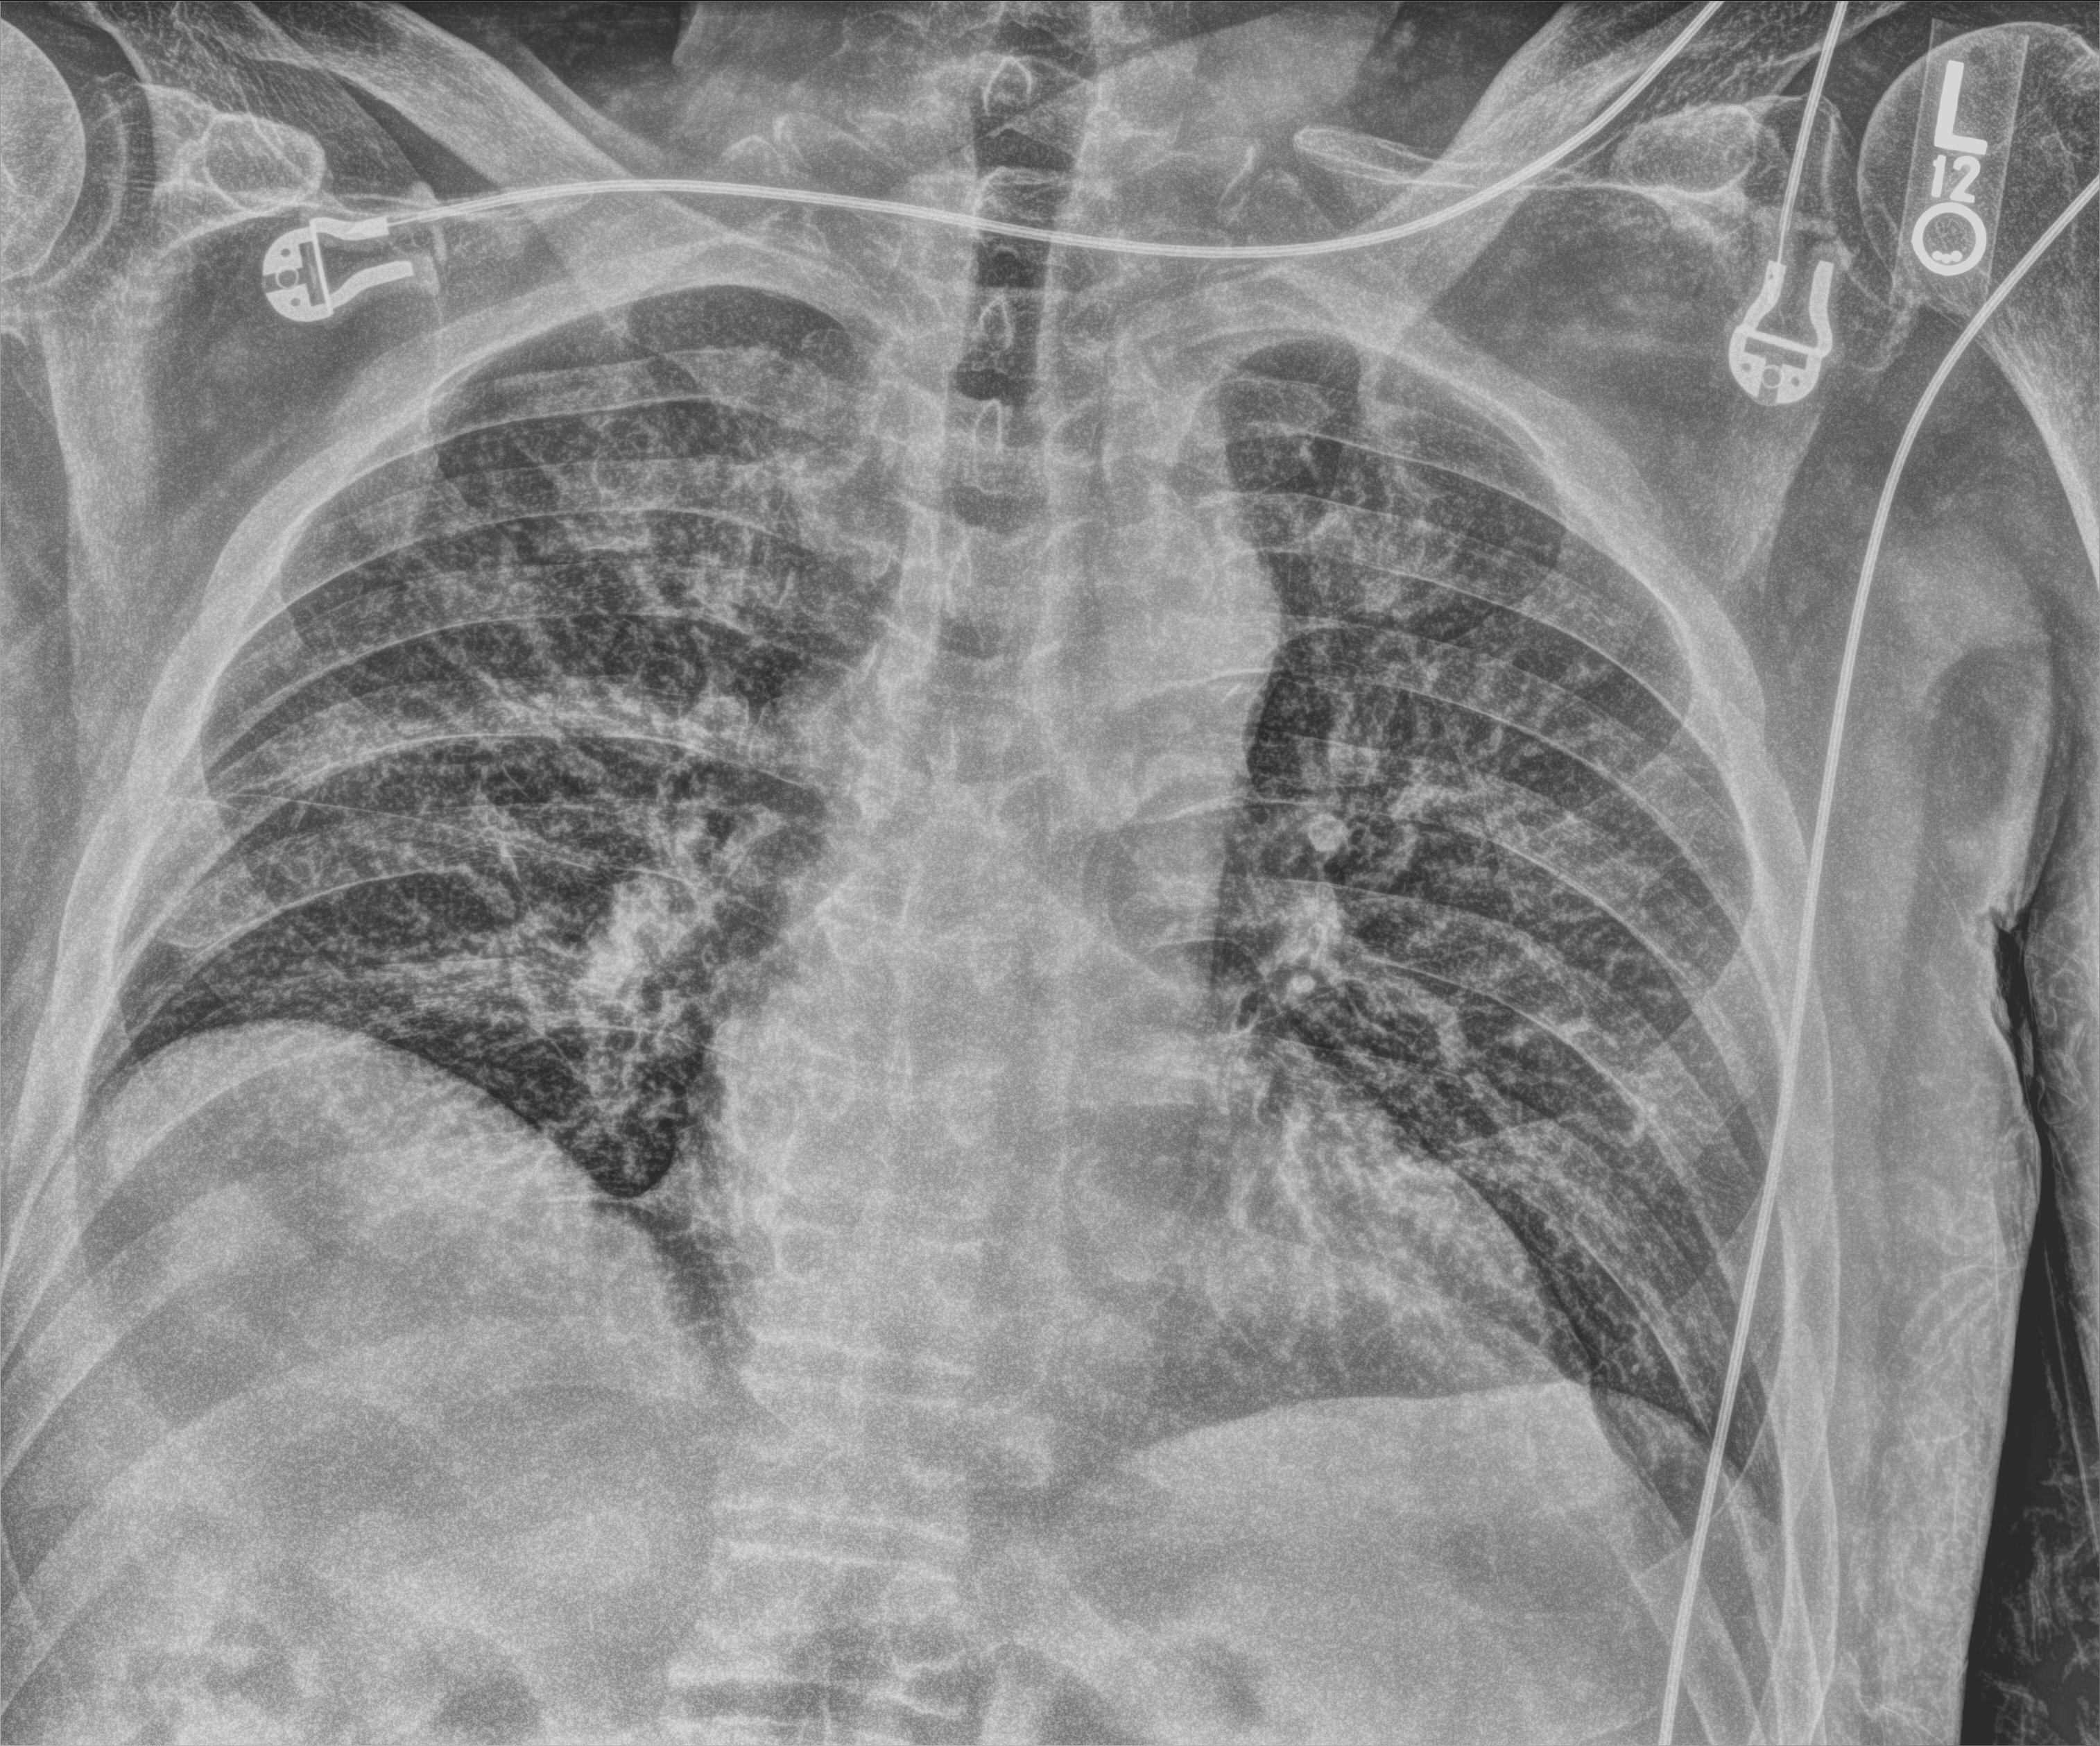
Chest X-ray (portable), anteroposterior (AP) projection. Patient hospitalised with COVID-19; male, aged 60–74 years.
From the hospital-stay record, not from the radiograph (when in the stay this image was taken is not recorded): mechanically ventilated during this hospital stay: no; length of hospital stay: 1 day; admitted to intensive care during this hospital stay: no.